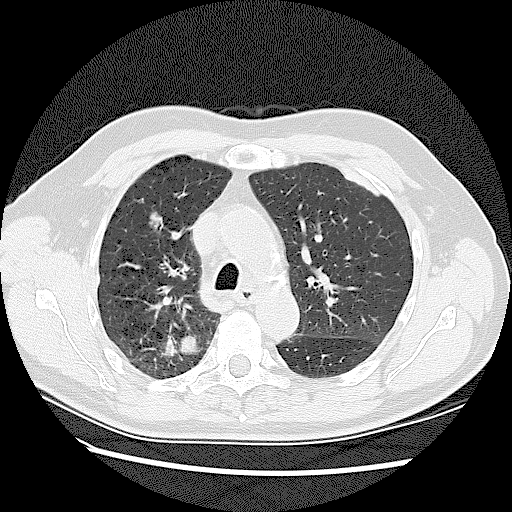
Low-dose screening chest CT, one axial slice. Position 88 of 128 along the scan axis. Reconstruction kernel LUNG. 120 kVp. Lung window (W 1500 / L -600 HU). 2.5 mm slice thickness. 512 × 512 image matrix, field of view 360 × 360 mm.
Structures marked on this image (manually delineated by an expert):
- lesion 1 (tumor, upper lobe of right lung): bounding box [x1, y1, x2, y2] px = [149, 213, 161, 227]
- lesion 2 (tumor, upper lobe of right lung): [179, 335, 198, 355]